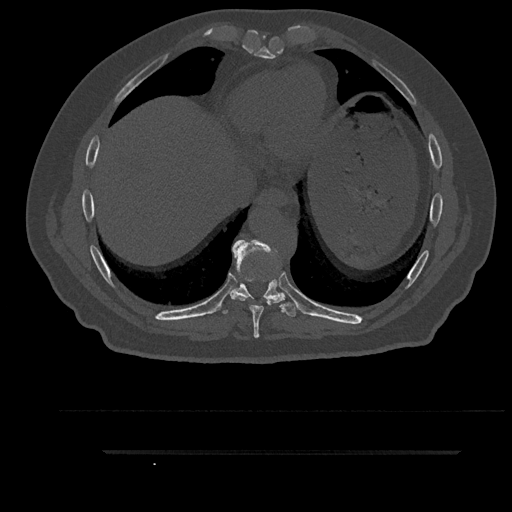
CT including the spine, one axial slice. Slice 448 of 797 in the series (ordered by position). 120 kVp. Bone window (W 1800 / L 400 HU). 512 × 512 image matrix, field of view 432 × 432 mm. Male patient, age 63 years. Case-level facts recorded for this patient, not image findings: primary cancer: renal.
Outlined on this slice (semi-automatic segmentation, software-assisted and operator-edited):
- T10 vertebra: bounding box [x1, y1, x2, y2] px = [281, 293, 285, 297]
- T8 vertebra: [231, 239, 281, 338]
- T9 vertebra: [215, 251, 296, 317]